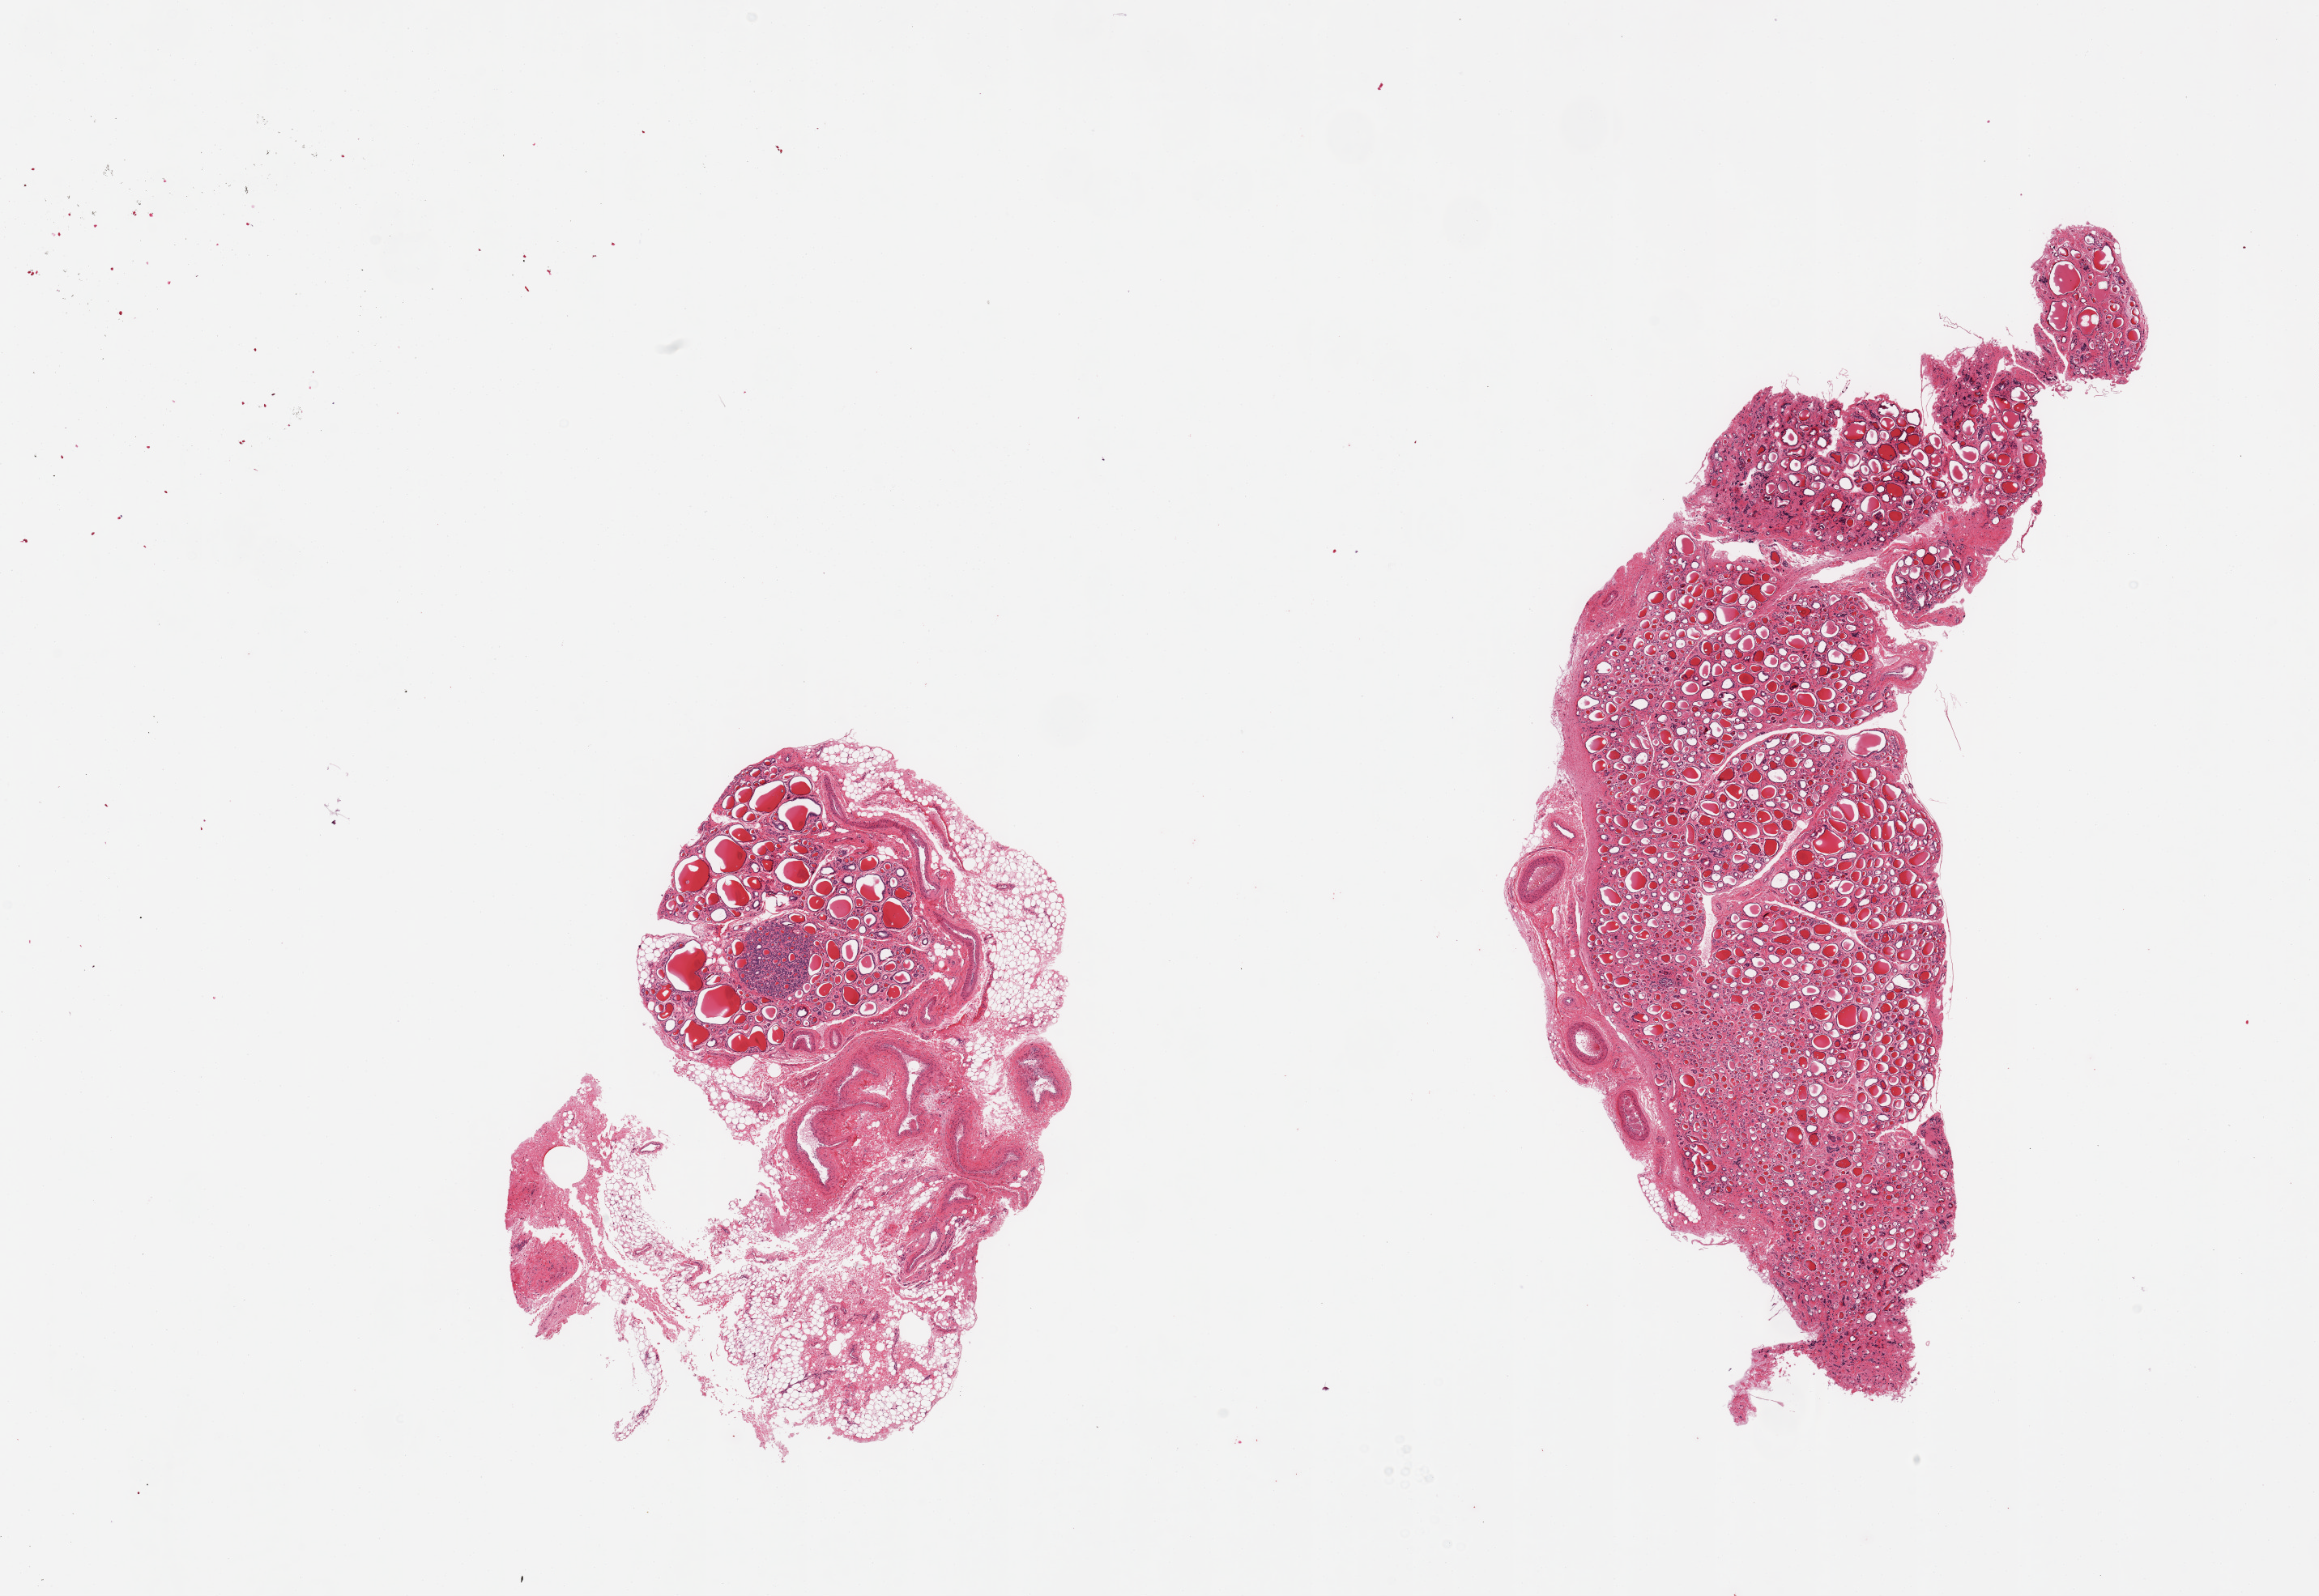
Whole-slide image, H&E stain, a low-resolution overview of the entire scanned area, about 22.6 x 15.6 mm, PAXgene-fixed, paraffin-embedded tissue, sampled site (target tissue): thyroid, tissue donor sample. Donor sex: female.
* review note (as recorded): 2 pieces; 1 piece has a 0.84 mm adenomatoid nodule (benign) or microadenoma. That piece has 50% fatty & vascular stroma